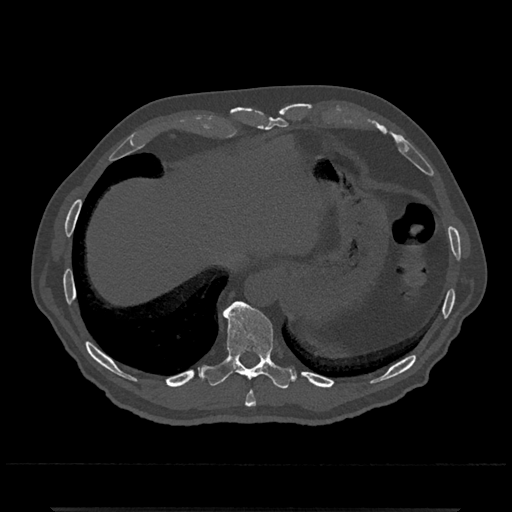
CT including the spine, one axial slice; position 560 of 797 along the scan axis; reconstruction kernel Br40s/3; bone window (W 1800 / L 400 HU); 0.5 mm slice thickness; 512 × 512 image matrix, field of view 393 × 393 mm. Male patient, age 67 years. From the clinical record (not read from this slice): primary cancer: prostate.
Annotated regions visible in this slice (semi-automatically segmented with operator editing):
- T10 vertebra: bounding box <203,301,294,389> (left, top, right, bottom; pixels)
- T9 vertebra: <245,391,256,407>